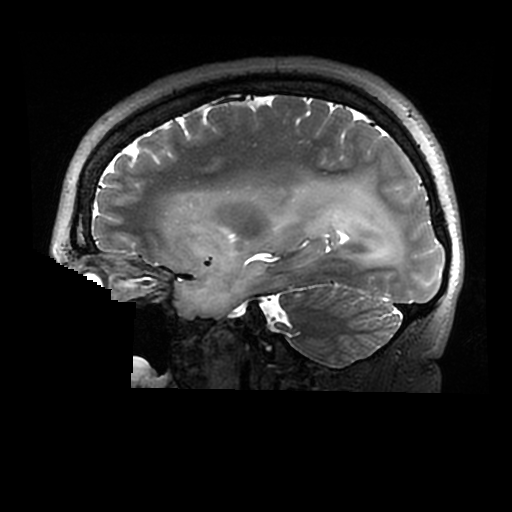
Brain MRI from a brain-tumour surgery series, one sagittal slice. Position 195 of 320 along the scan axis. 512 × 512 image matrix. Case-level facts recorded for this patient, not image findings: histopathology: Astrocytoma; WHO grade: 2; IDH mutation: yes.
Structures marked on this image (expert manual segmentation):
- tumour: bounding box [x1, y1, x2, y2] px = [174, 183, 404, 319]